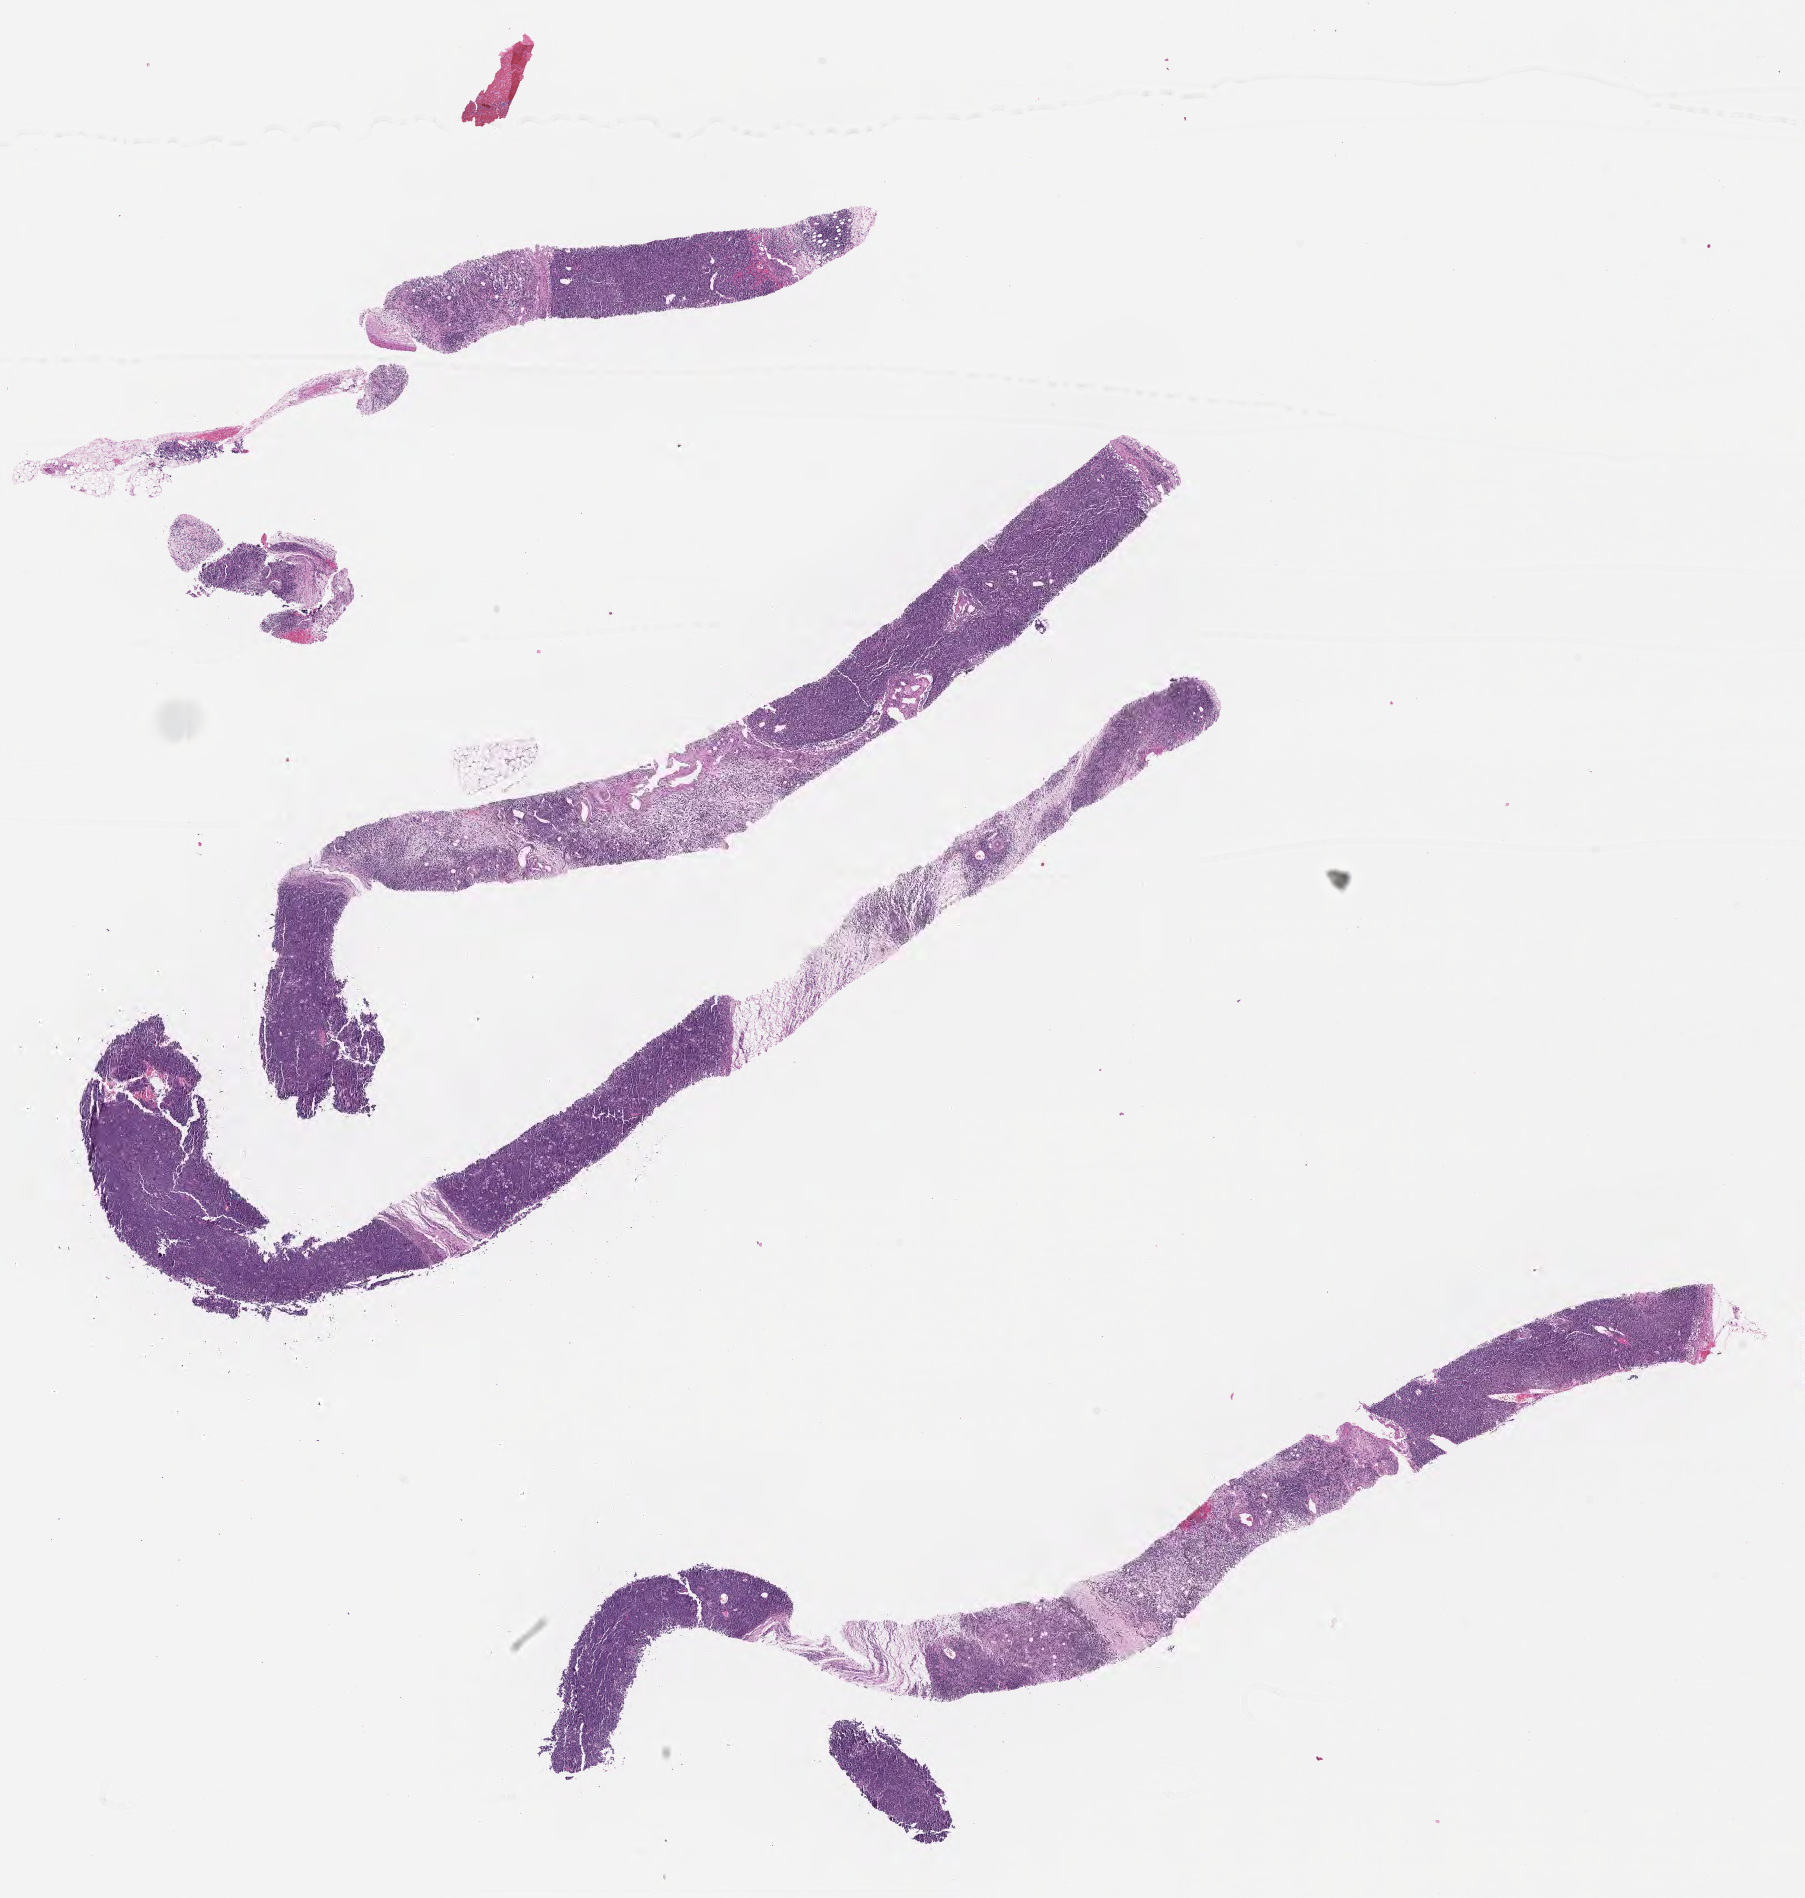
Haematoxylin and eosin whole-slide image, a low-resolution overview of the entire scanned area, about 14.6 x 15.3 mm. FFPE section. Specimen: primary tumor. Patient: male, 47 years old. Pathologist review of this section (percent, as recorded): tumor cells 70%, tumor nuclei 90%, stromal cells 25%, necrosis 5%, normal cells 0%. Inflammatory infiltration, as recorded: lymphocyte infiltration 50%, monocyte infiltration 25%, neutrophil infiltration 5%.
- Ann Arbor stage (patient): Stage IV
- diagnosis: Burkitt lymphoma, NOS
- section: top of the tissue portion